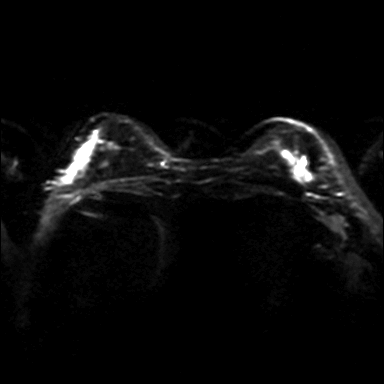
Breast MRI, one axial slice; position 8 of 36 along the scan axis; diffusion-weighted series; image 2 of 4 stored at this slice position (different b-values; order by instance number); 3 T; 4 mm slice thickness; 384 × 384 image matrix. Female patient.
Annotated regions visible in this slice (outlined manually by an expert reader):
- tumour on diffusion-weighted imaging: bounding box [x1, y1, x2, y2] px = [301, 169, 307, 176]